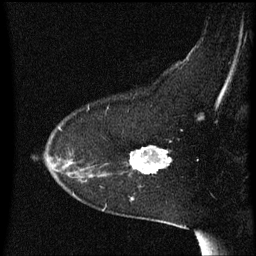
Breast MRI (dynamic contrast-enhanced), one sagittal slice. Dynamic contrast-enhanced series, image 2 of 3 at this slice position (ordered by acquisition). 1.5 T. TE 4.2 ms, TR 8.4 ms. 2 mm slice thickness. 256 × 256 image matrix, field of view 200 × 200 mm. Patient: female, 54 years. From the clinical record (not read from this slice): setting: breast cancer imaged before/during neoadjuvant chemotherapy; receptor status: HR-positive, HER2-negative.
Outlined on this slice (semi-automatically segmented with operator editing):
- analysis volume of interest (the breast-tissue region the enhancement analysis was run in; not a lesion): bounding box <118,146,172,185> (left, top, right, bottom; pixels)
- tumour enhancement mask (voxels above the 70 % enhancement threshold inside the analysis volume of interest): <131,146,172,175>